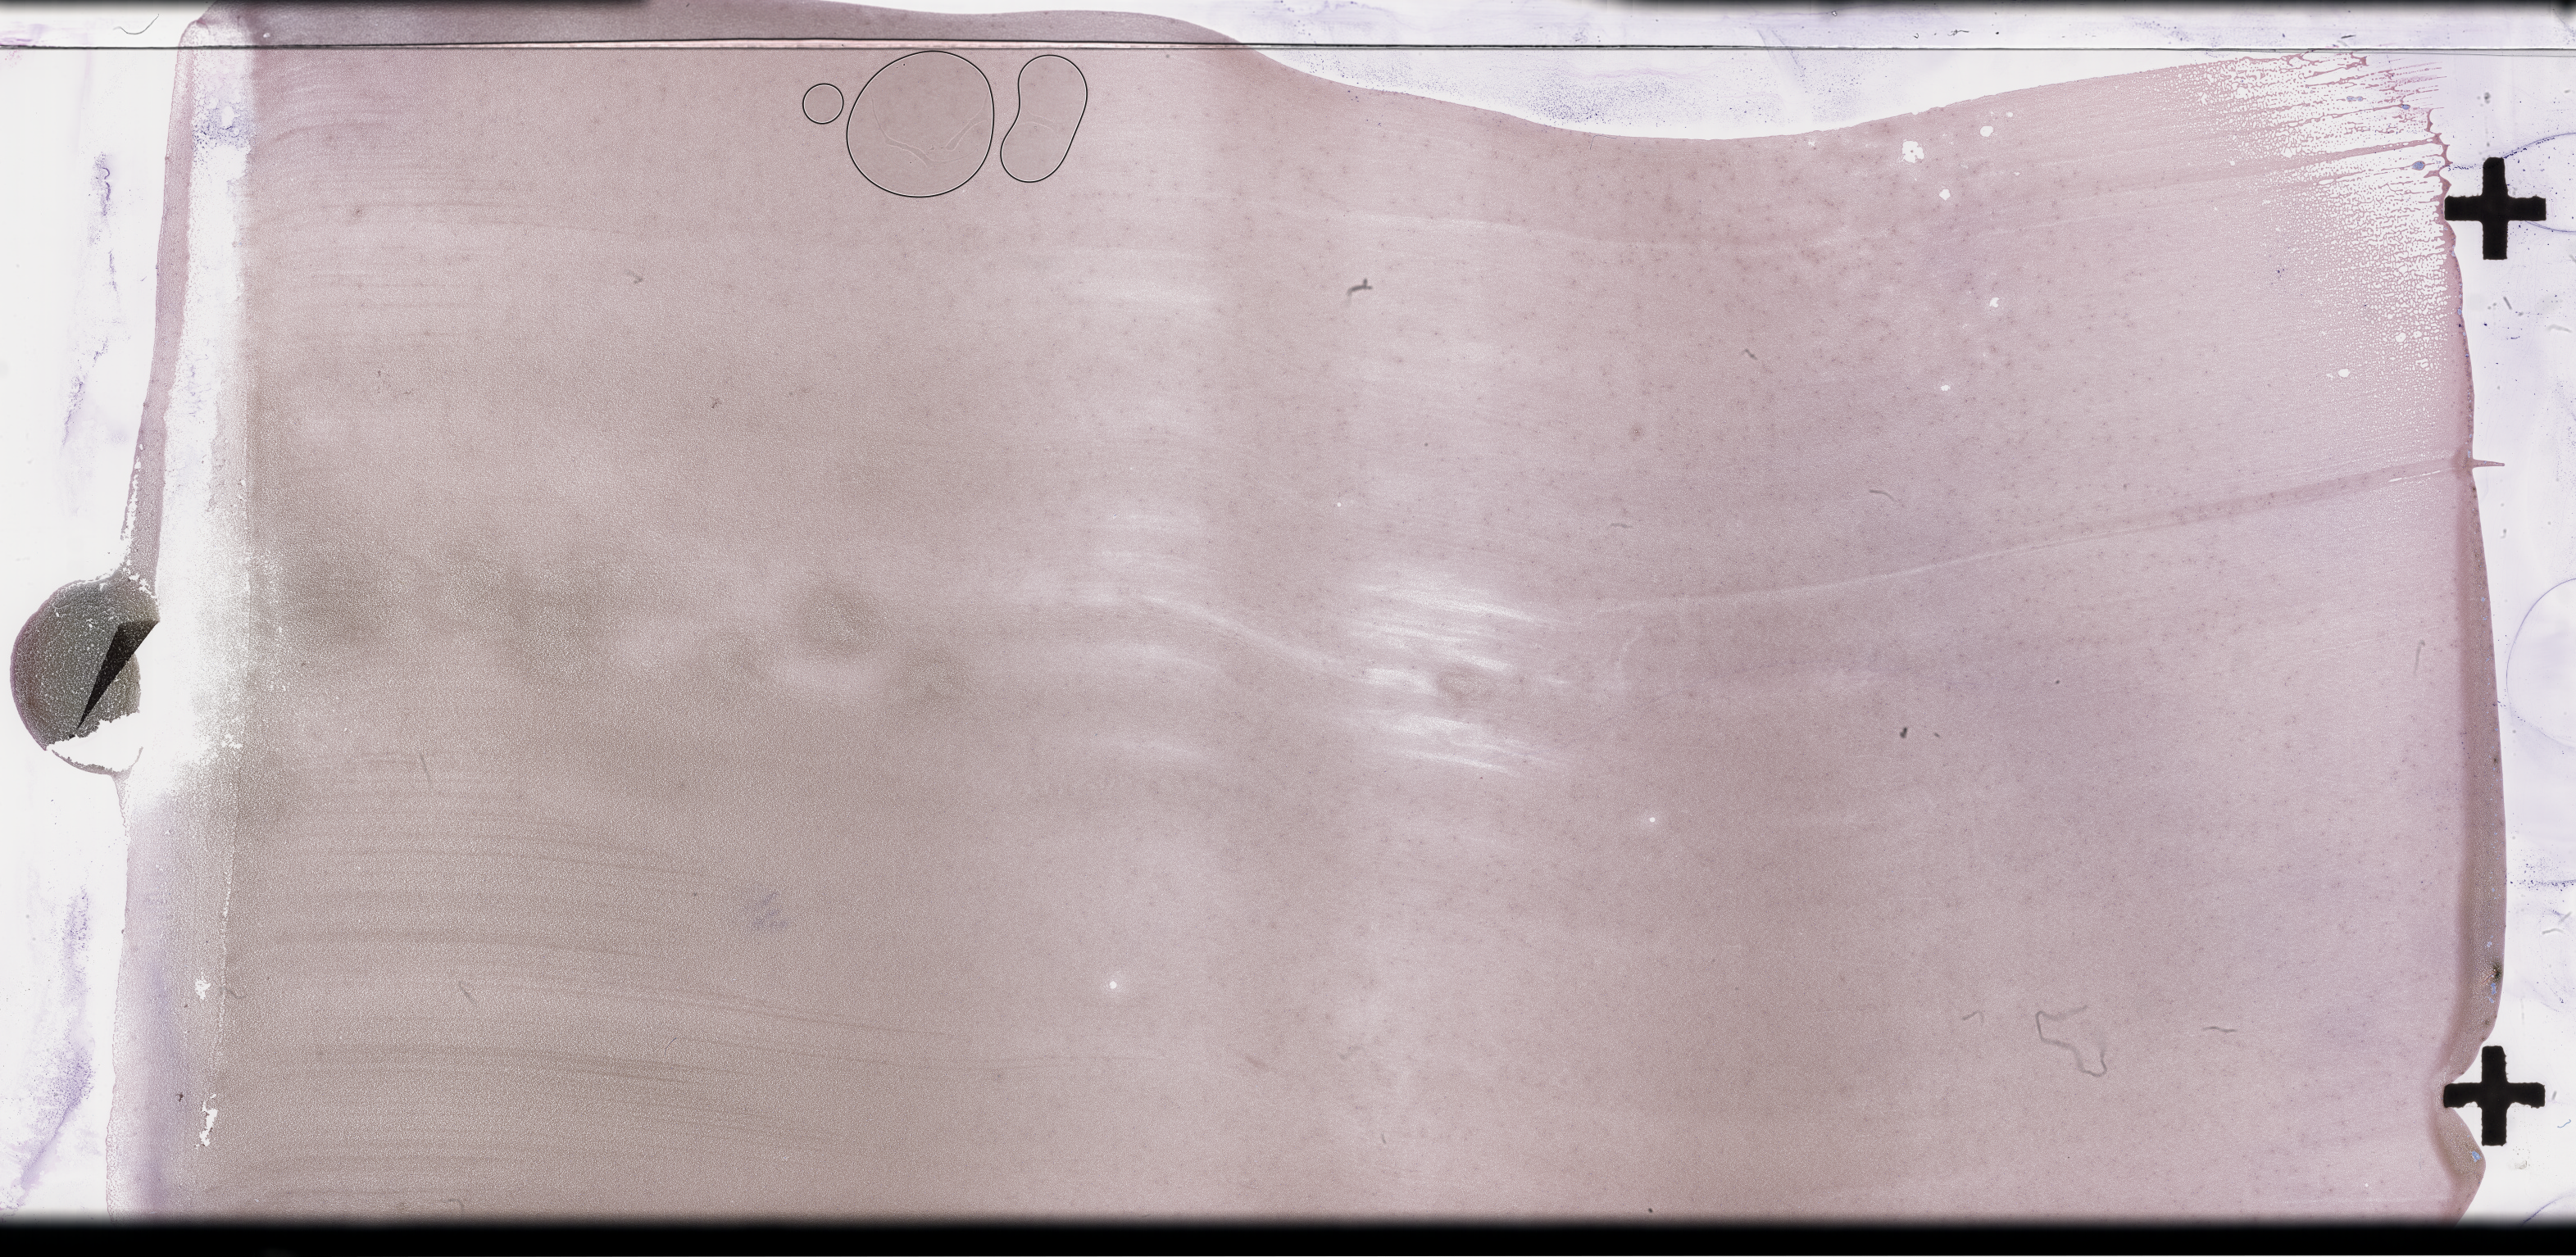
Wright–Giemsa-stained whole blood smear, whole-slide image — a low-resolution overview of the entire scanned area, about 50.8 x 24.8 mm. EDTA-anticoagulated smear. Patient: male.
Patient diagnosis: Plasma Cell Myeloma.